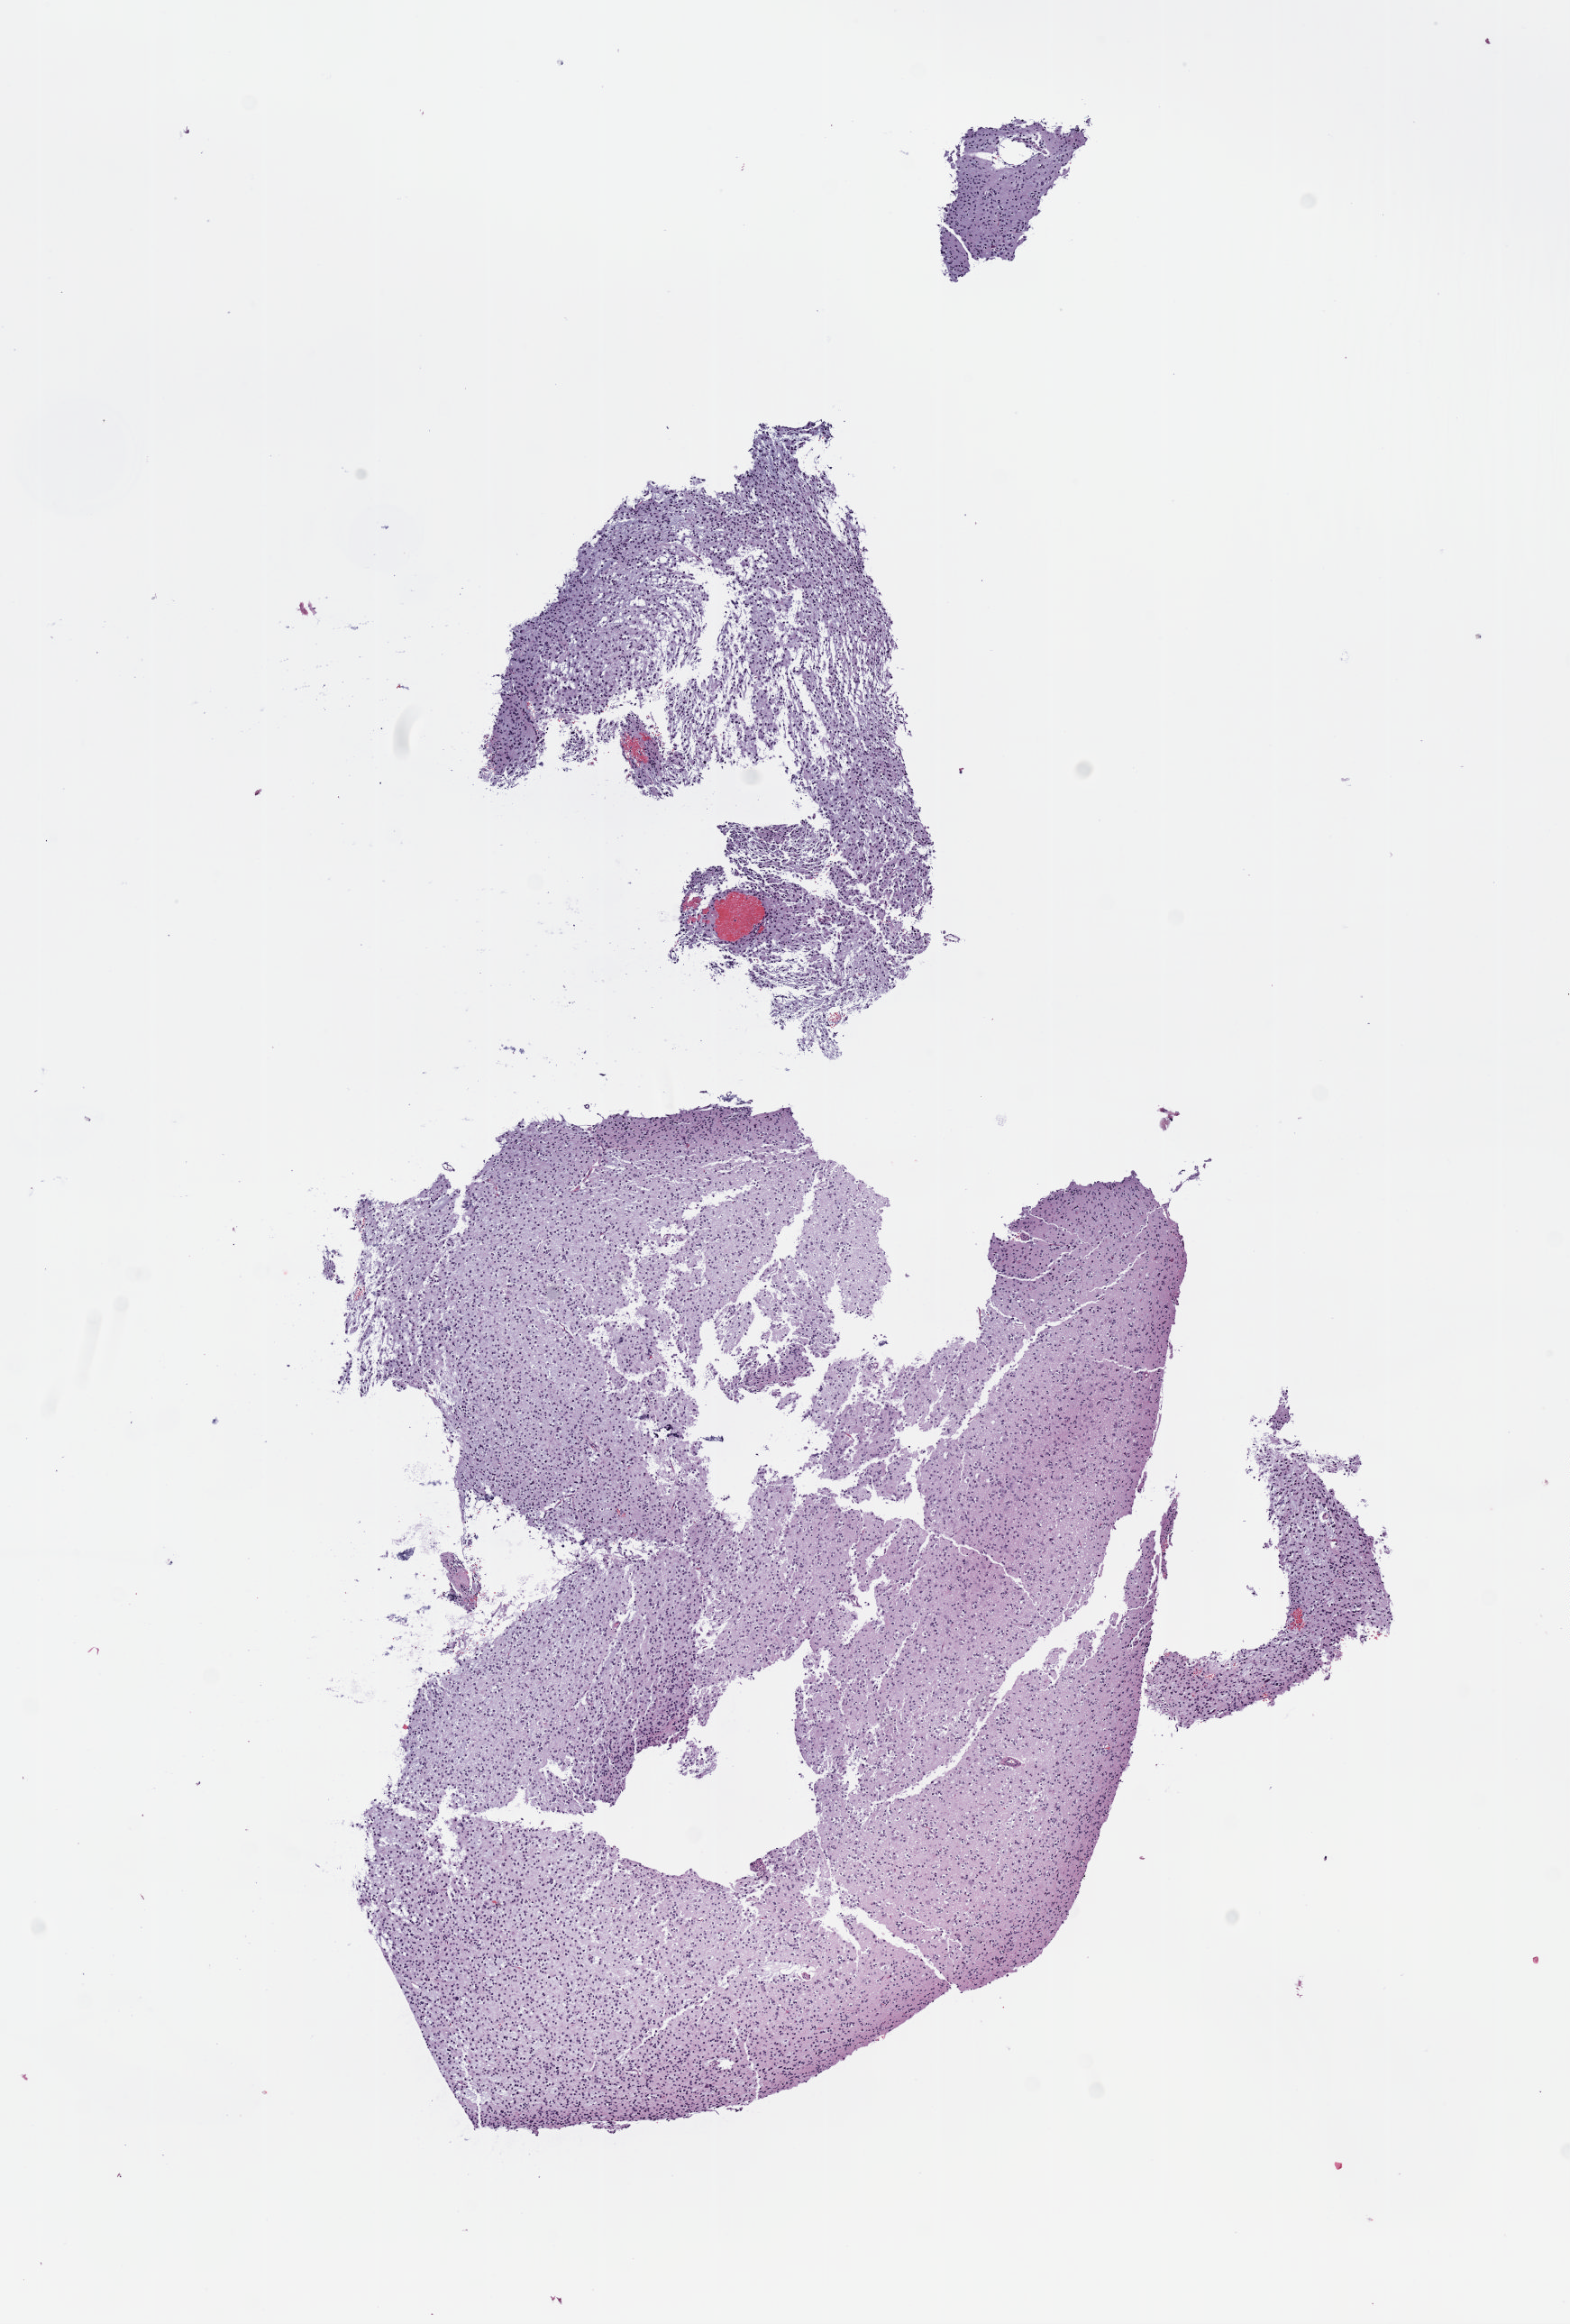
H&E whole-slide image — whole scanned area (about 7.0 x 10.4 mm, acquisition: 40x scan) shown as a low-resolution overview. Formalin-fixed paraffin-embedded (FFPE) diagnostic section. Brain, primary tumour sample. Female, age 50 years at initial diagnosis. Histologic grade: G2 (moderately differentiated).
* laterality: right
* pathologic diagnosis: Oligodendroglioma, NOS (cerebrum)